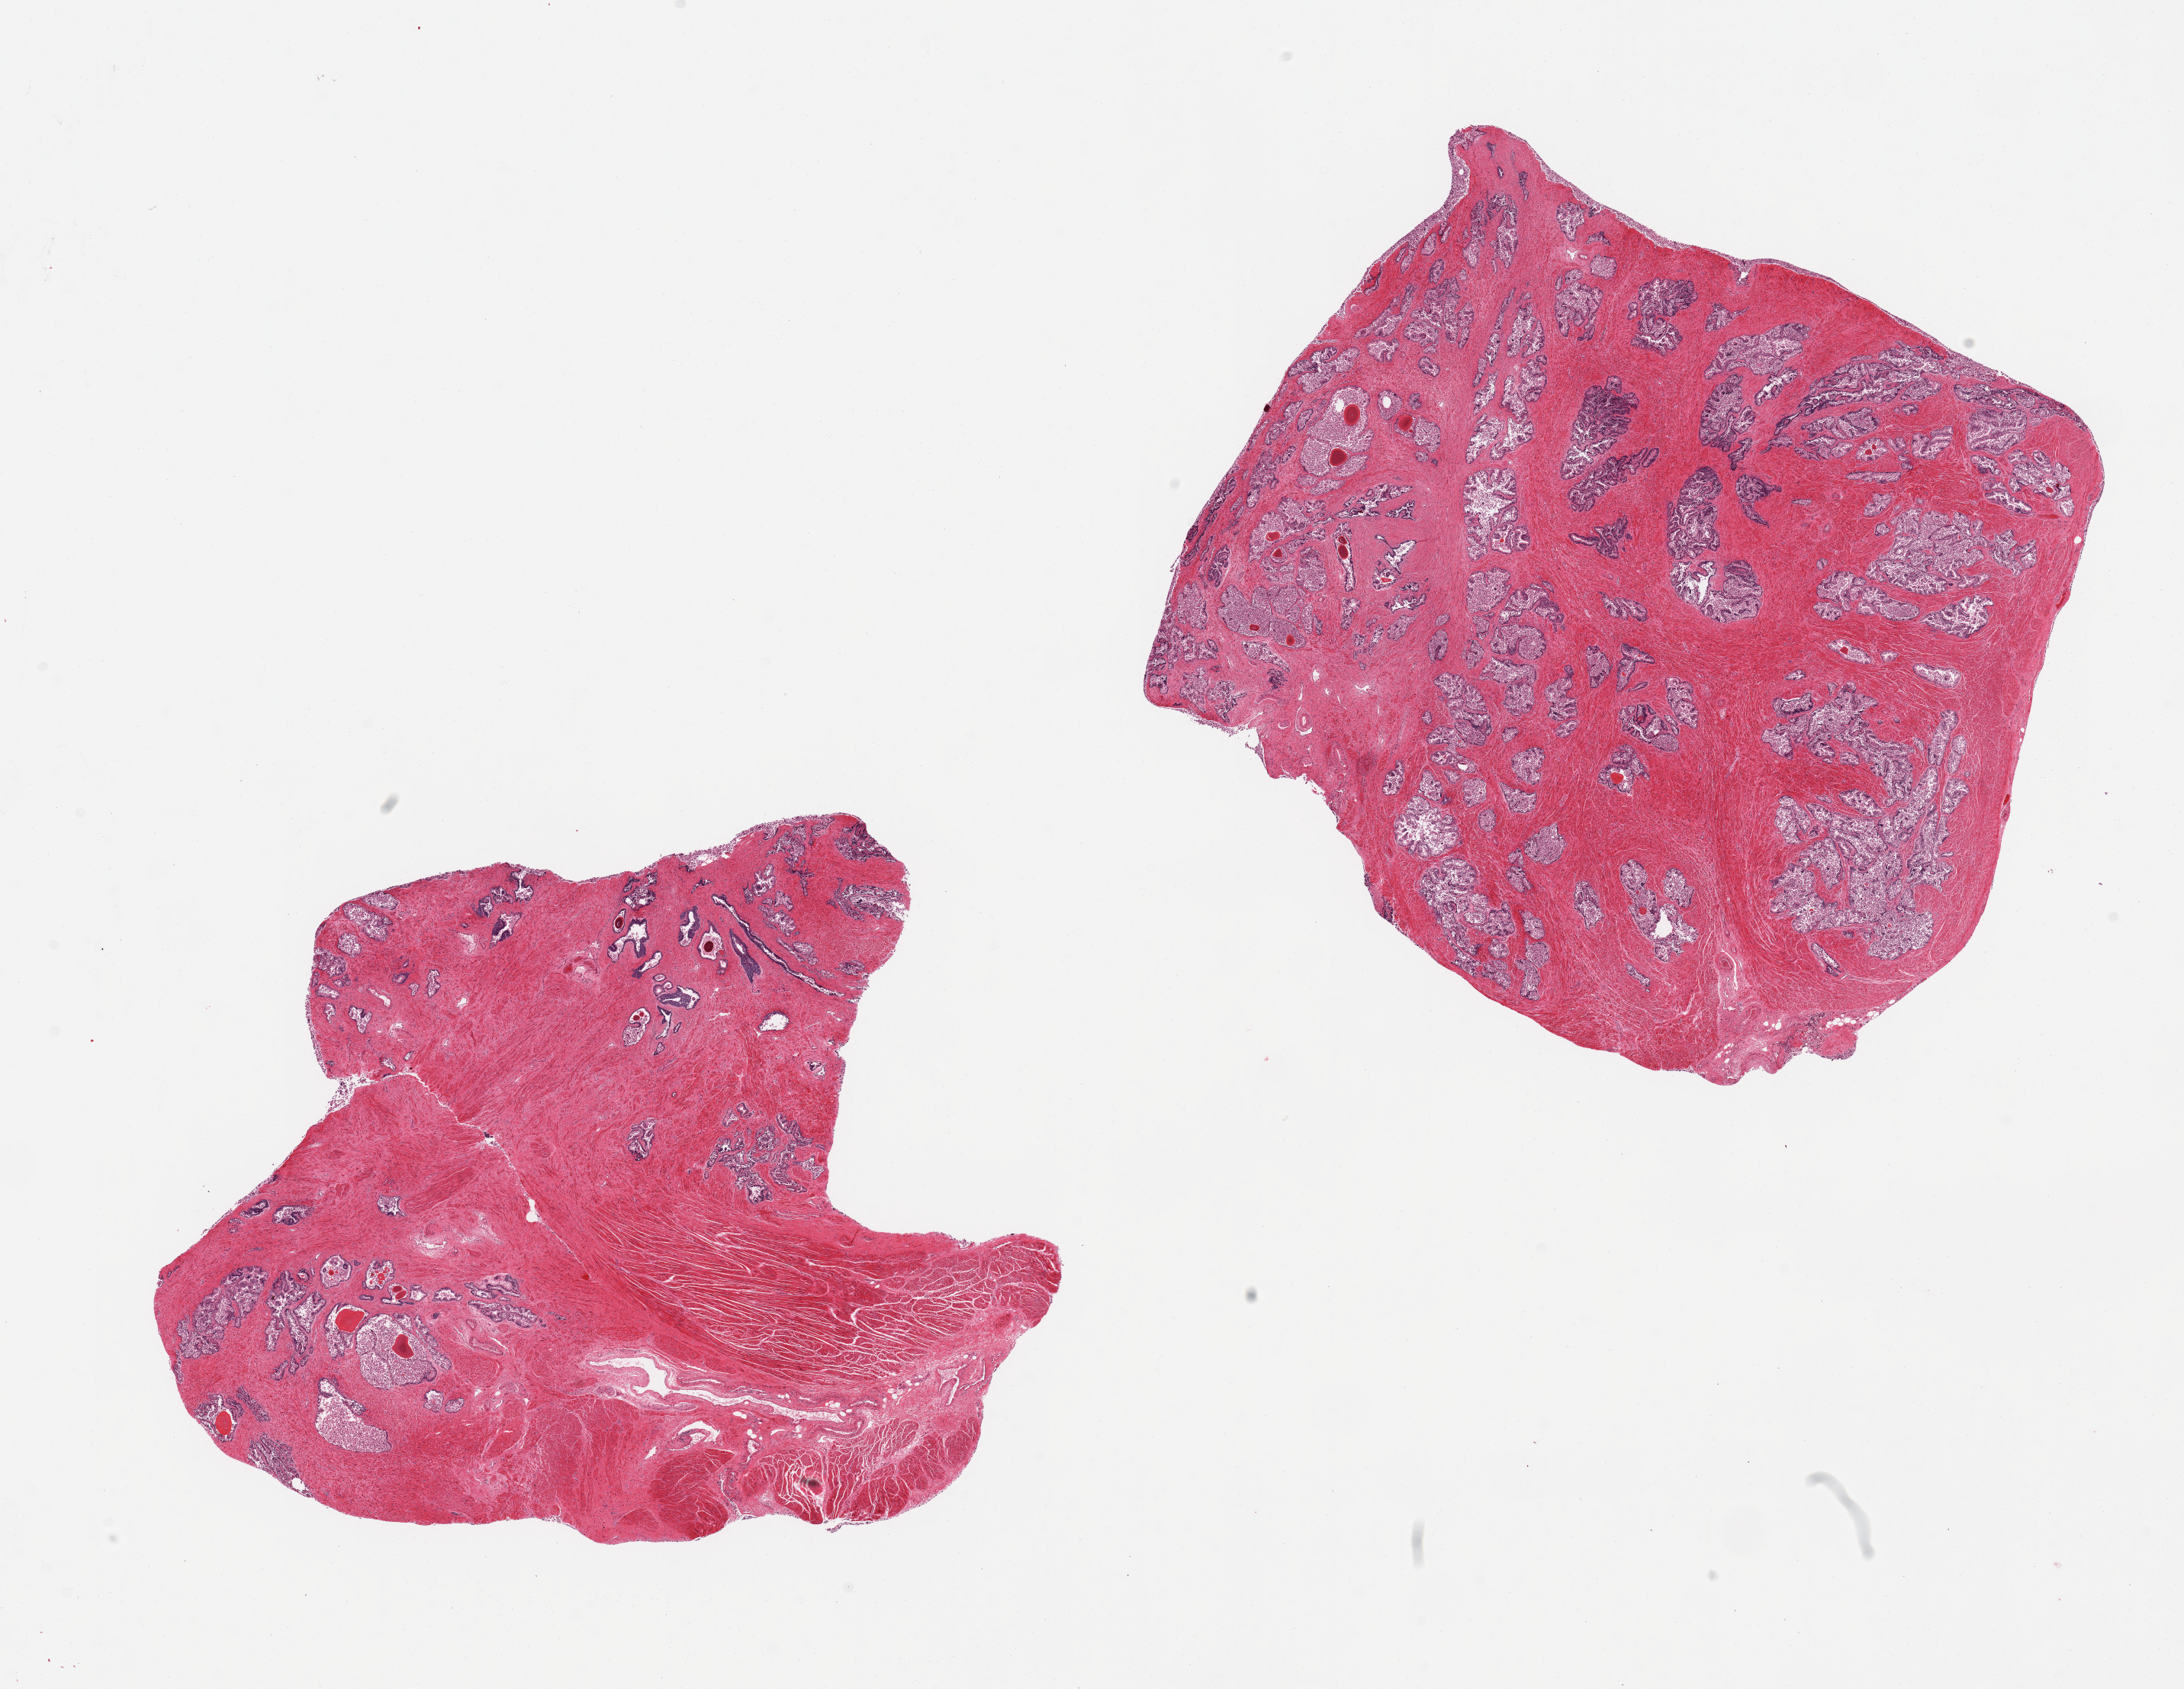
Digitized haematoxylin and eosin-stained section, brightfield, whole scanned area (about 22.6 x 17.5 mm, acquisition: 20x scan) shown as a low-resolution overview, PAXgene-fixed, paraffin-embedded tissue, target tissue: prostate, donor tissue sample. Donor: male.
• reviewer comment on this tissue sample: 2 pieces, epithelium sloughing, glandular hyperplastic pattern